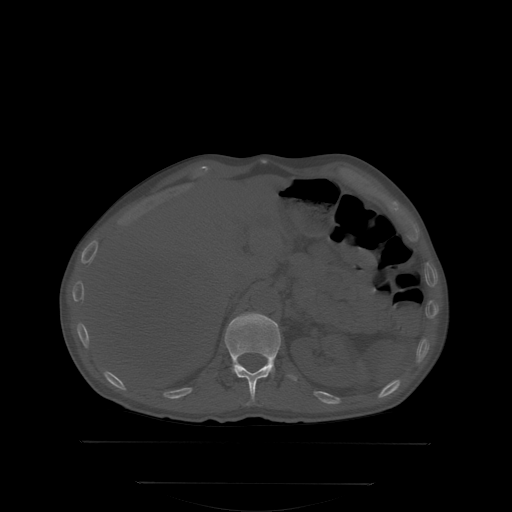
CT including the spine, one axial slice. Position 166 of 350 along the scan axis. Bone window (W 1800 / L 400 HU). 2.5 mm slice thickness. 512 × 512 image matrix, field of view 500 × 500 mm. Male patient, age 58 years. From the clinical record (not read from this slice): primary cancer: prostate; vertebrae with lytic lesions (as recorded): L1.
Annotated regions visible in this slice (semi-automatically segmented with operator editing):
- T12 vertebra: bounding box <225,314,281,405> (left, top, right, bottom; pixels)